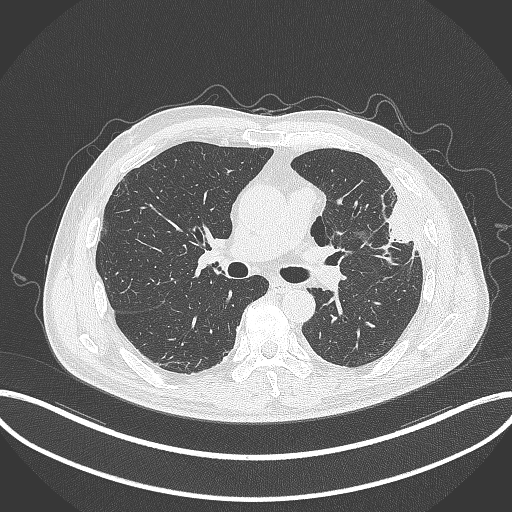
Chest CT, one axial slice. Slice 195 of 382 in the series (ordered by position). Reconstruction kernel B70f. 120 kVp. Lung window (W 1500 / L -600 HU). 512 × 512 image matrix, field of view 415 × 415 mm. Patient: male, 64 years. From the clinical record (not read from this slice): clinical TNM (as recorded): T4 N1 M0.
Annotated regions visible in this slice (bounding box drawn by a radiologist):
- lung tumour (recorded histology: adenocarcinoma): bounding box <372,184,422,259> (left, top, right, bottom; pixels)